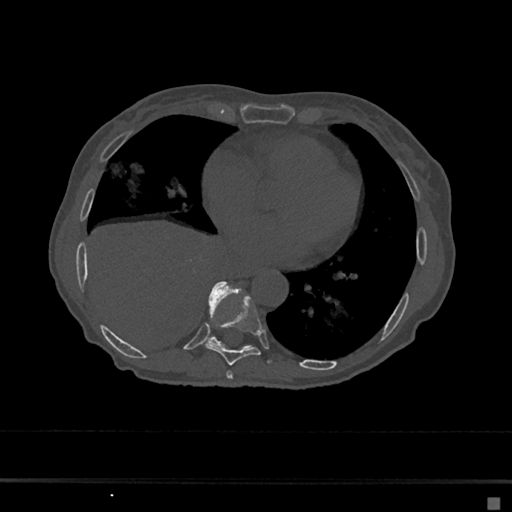
CT including the spine, one axial slice. Slice 309 of 797 in the series (ordered by position). Reconstruction kernel Br40s/3. Bone window (W 1800 / L 400 HU). 512 × 512 image matrix, field of view 360 × 360 mm. Female patient, age 68 years. From the clinical record (not read from this slice): primary cancer: renal.
Annotated regions visible in this slice (semi-automatic segmentation, software-assisted and operator-edited):
- T7 vertebra: bounding box [x1, y1, x2, y2] px = [226, 371, 233, 379]
- T8 vertebra: [205, 294, 272, 366]
- T9 vertebra: [208, 281, 250, 348]